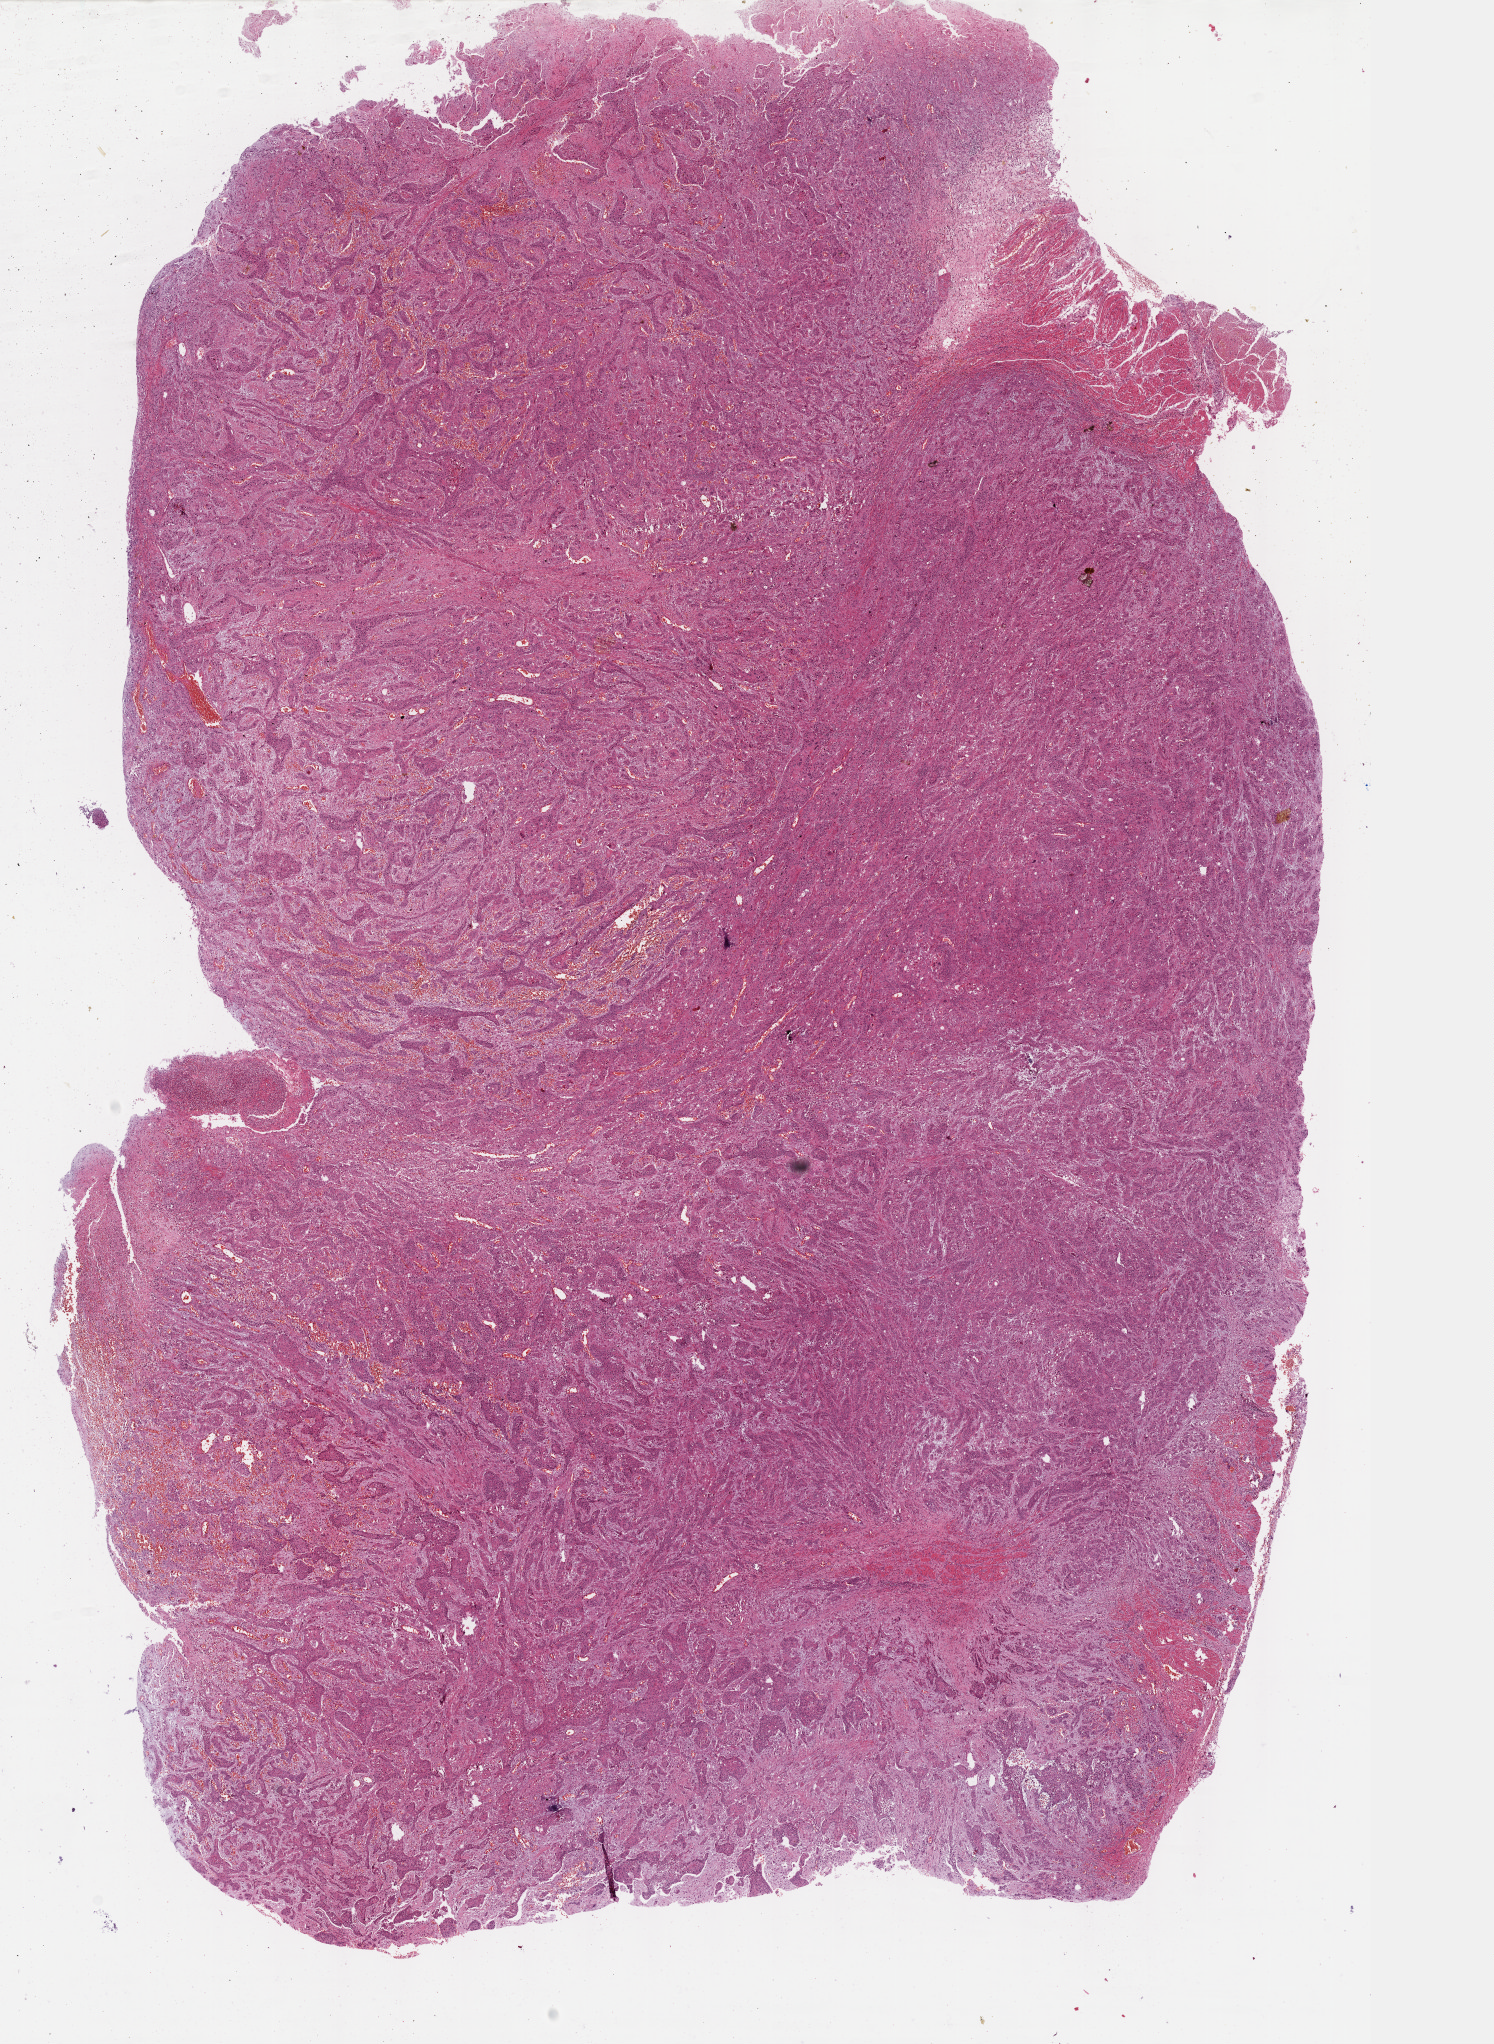
Digitized H&E-stained tissue section (whole slide) — a low-resolution overview of the entire scanned area, about 12.1 x 16.5 mm (acquisition: 40x scan), formalin-fixed paraffin-embedded (FFPE) diagnostic section, primary tumour sample from the esophagus. Male patient; age at initial diagnosis 70 years. Histologic grade: G2 (moderately differentiated).
Diagnosis: Squamous cell carcinoma, NOS (upper third of esophagus). AJCC pathologic stage: IIB. Lymph nodes positive (case pathology): 1 of 2 examined.